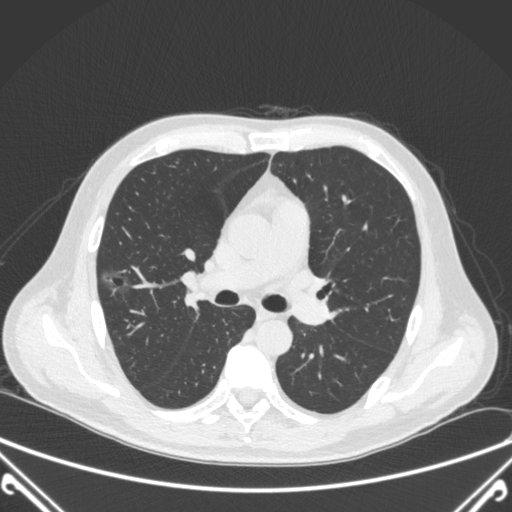
Chest CT, one axial slice; position 223 of 360 along the scan axis; lung window (W 1500 / L -600 HU); 1 mm slice thickness; 512 × 512 image matrix. Male patient, age 64 years. From the clinical record (not read from this slice): clinical TNM (as recorded): T1c N0 M0.
Structures marked on this image (rectangle marked by the reading radiologist):
- lung tumour (recorded histology: adenocarcinoma): box from (x=98, y=265) to (x=142, y=303) px